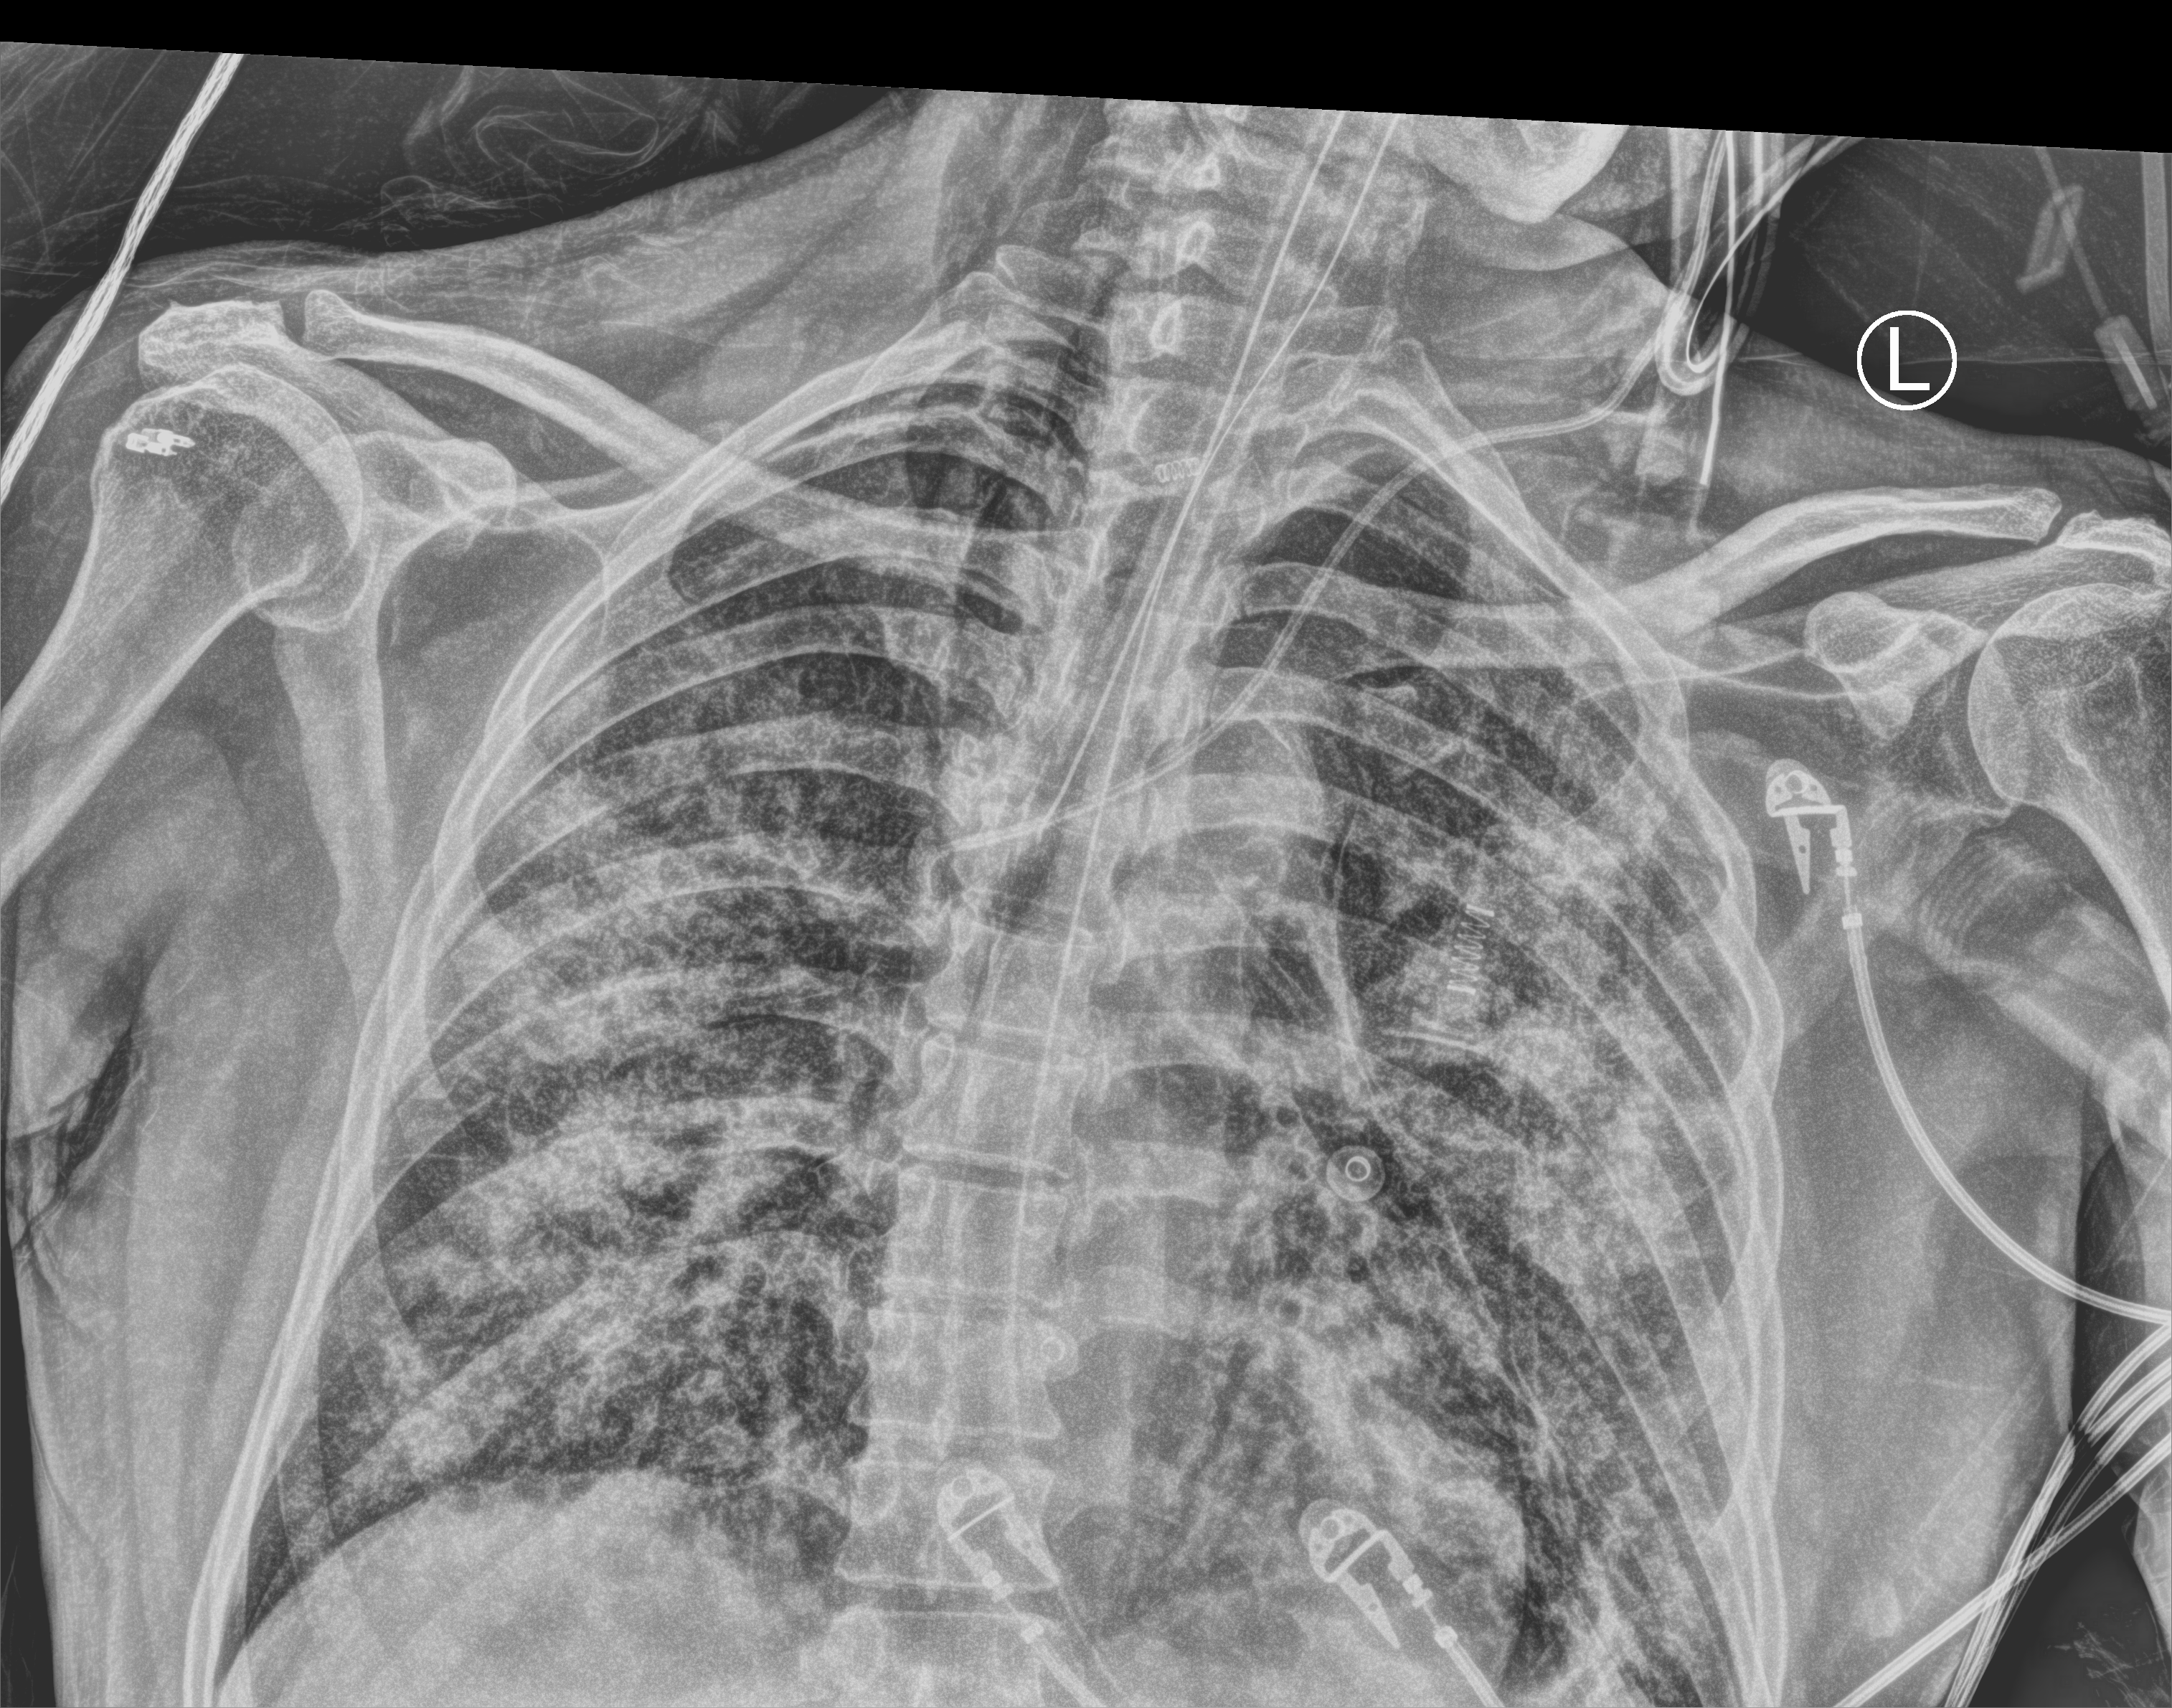
Bedside chest radiograph (computed radiography). Patient hospitalised with COVID-19; male, aged 60–74 years.
Admission-level facts for this patient (not findings on this image; timing relative to this image not recorded): mechanically ventilated during this hospital stay: yes; admitted to intensive care during this hospital stay: yes; COPD (admission record): no.